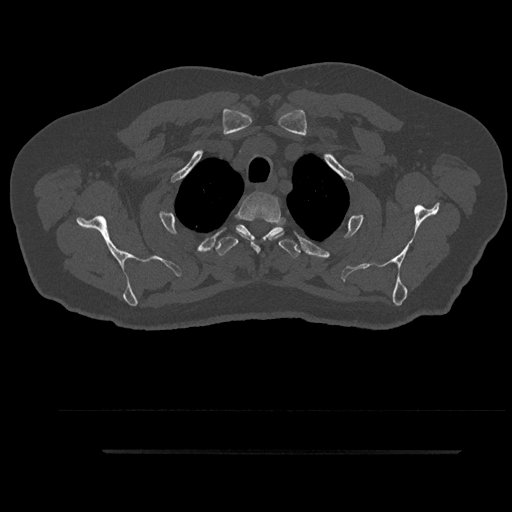
CT including the spine, one axial slice; position 741 of 797 along the scan axis; reconstruction kernel Br40s/3; bone window (W 1800 / L 400 HU); 512 × 512 image matrix, field of view 432 × 432 mm. Male patient, age 63 years. Case-level facts recorded for this patient, not image findings: primary cancer: renal; vertebrae with lytic lesions (as recorded): T8.
Structures marked on this image (semi-automatic segmentation, software-assisted and operator-edited):
- T2 vertebra: bounding box (x1, y1, x2, y2) in pixels: (237, 191, 284, 252)
- T3 vertebra: (215, 224, 301, 258)